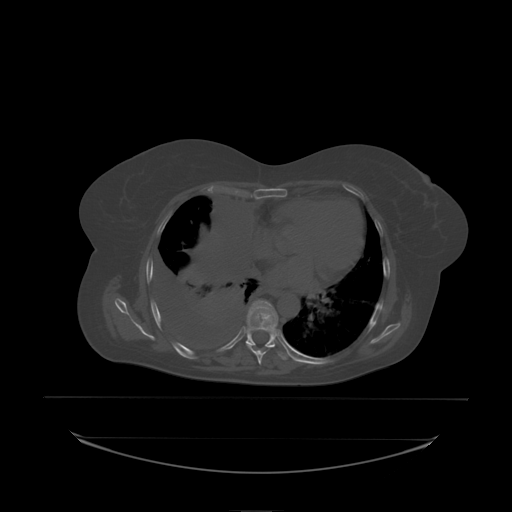
CT including the spine, one axial slice; slice 137 of 242 in the series (ordered by position); bone window (W 1800 / L 400 HU); 2.5 mm slice thickness; 512 × 512 image matrix. Female patient, age 53 years. Case-level facts recorded for this patient, not image findings: primary cancer: lung; vertebrae with lytic lesions (as recorded): T7, L1.
Annotated regions visible in this slice (semi-automatically segmented with operator editing):
- T7 vertebra: bounding box (x1, y1, x2, y2) in pixels: (249, 308, 251, 311)
- T8 vertebra: (247, 300, 278, 338)